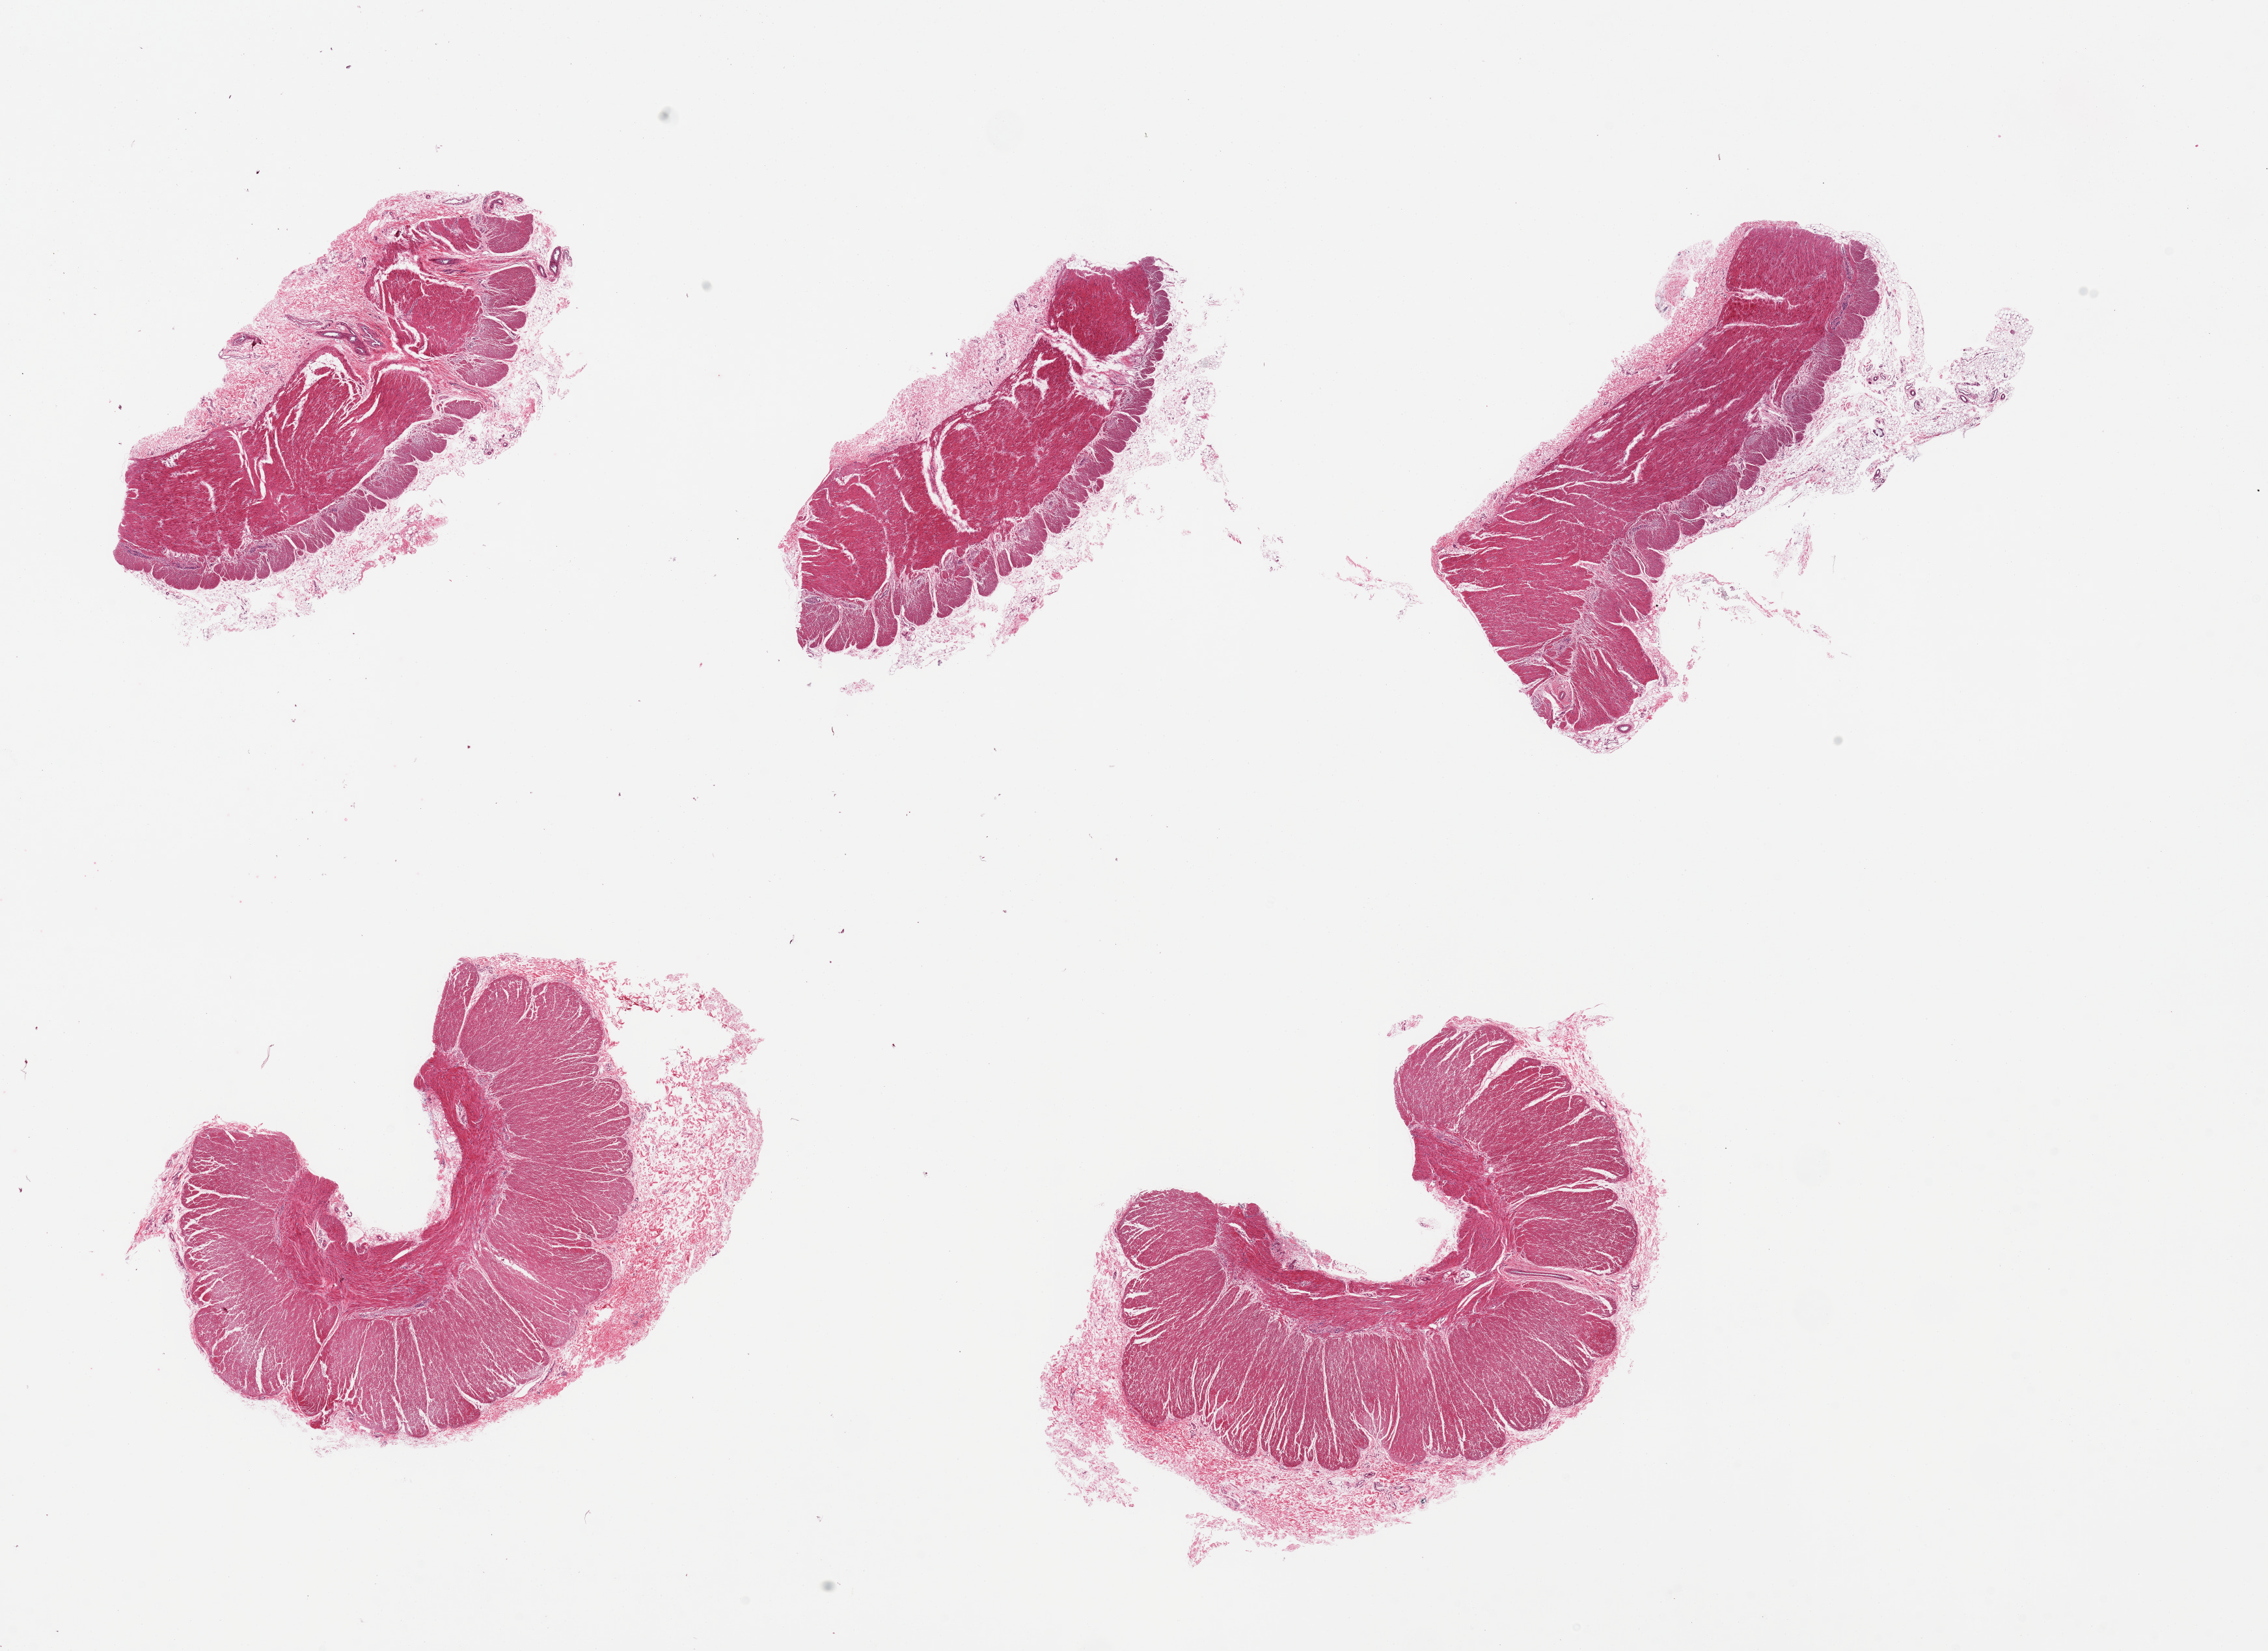
Haematoxylin and eosin whole-slide image, a low-resolution overview of the entire scanned area, about 27.6 x 20.1 mm (from a 20x scan). PAXgene-fixed, paraffin-embedded tissue. Sampled site (target tissue): sigmoid colon. Donor tissue sample. Female donor.
Review note (as recorded): 5 pieces, well trimmed.